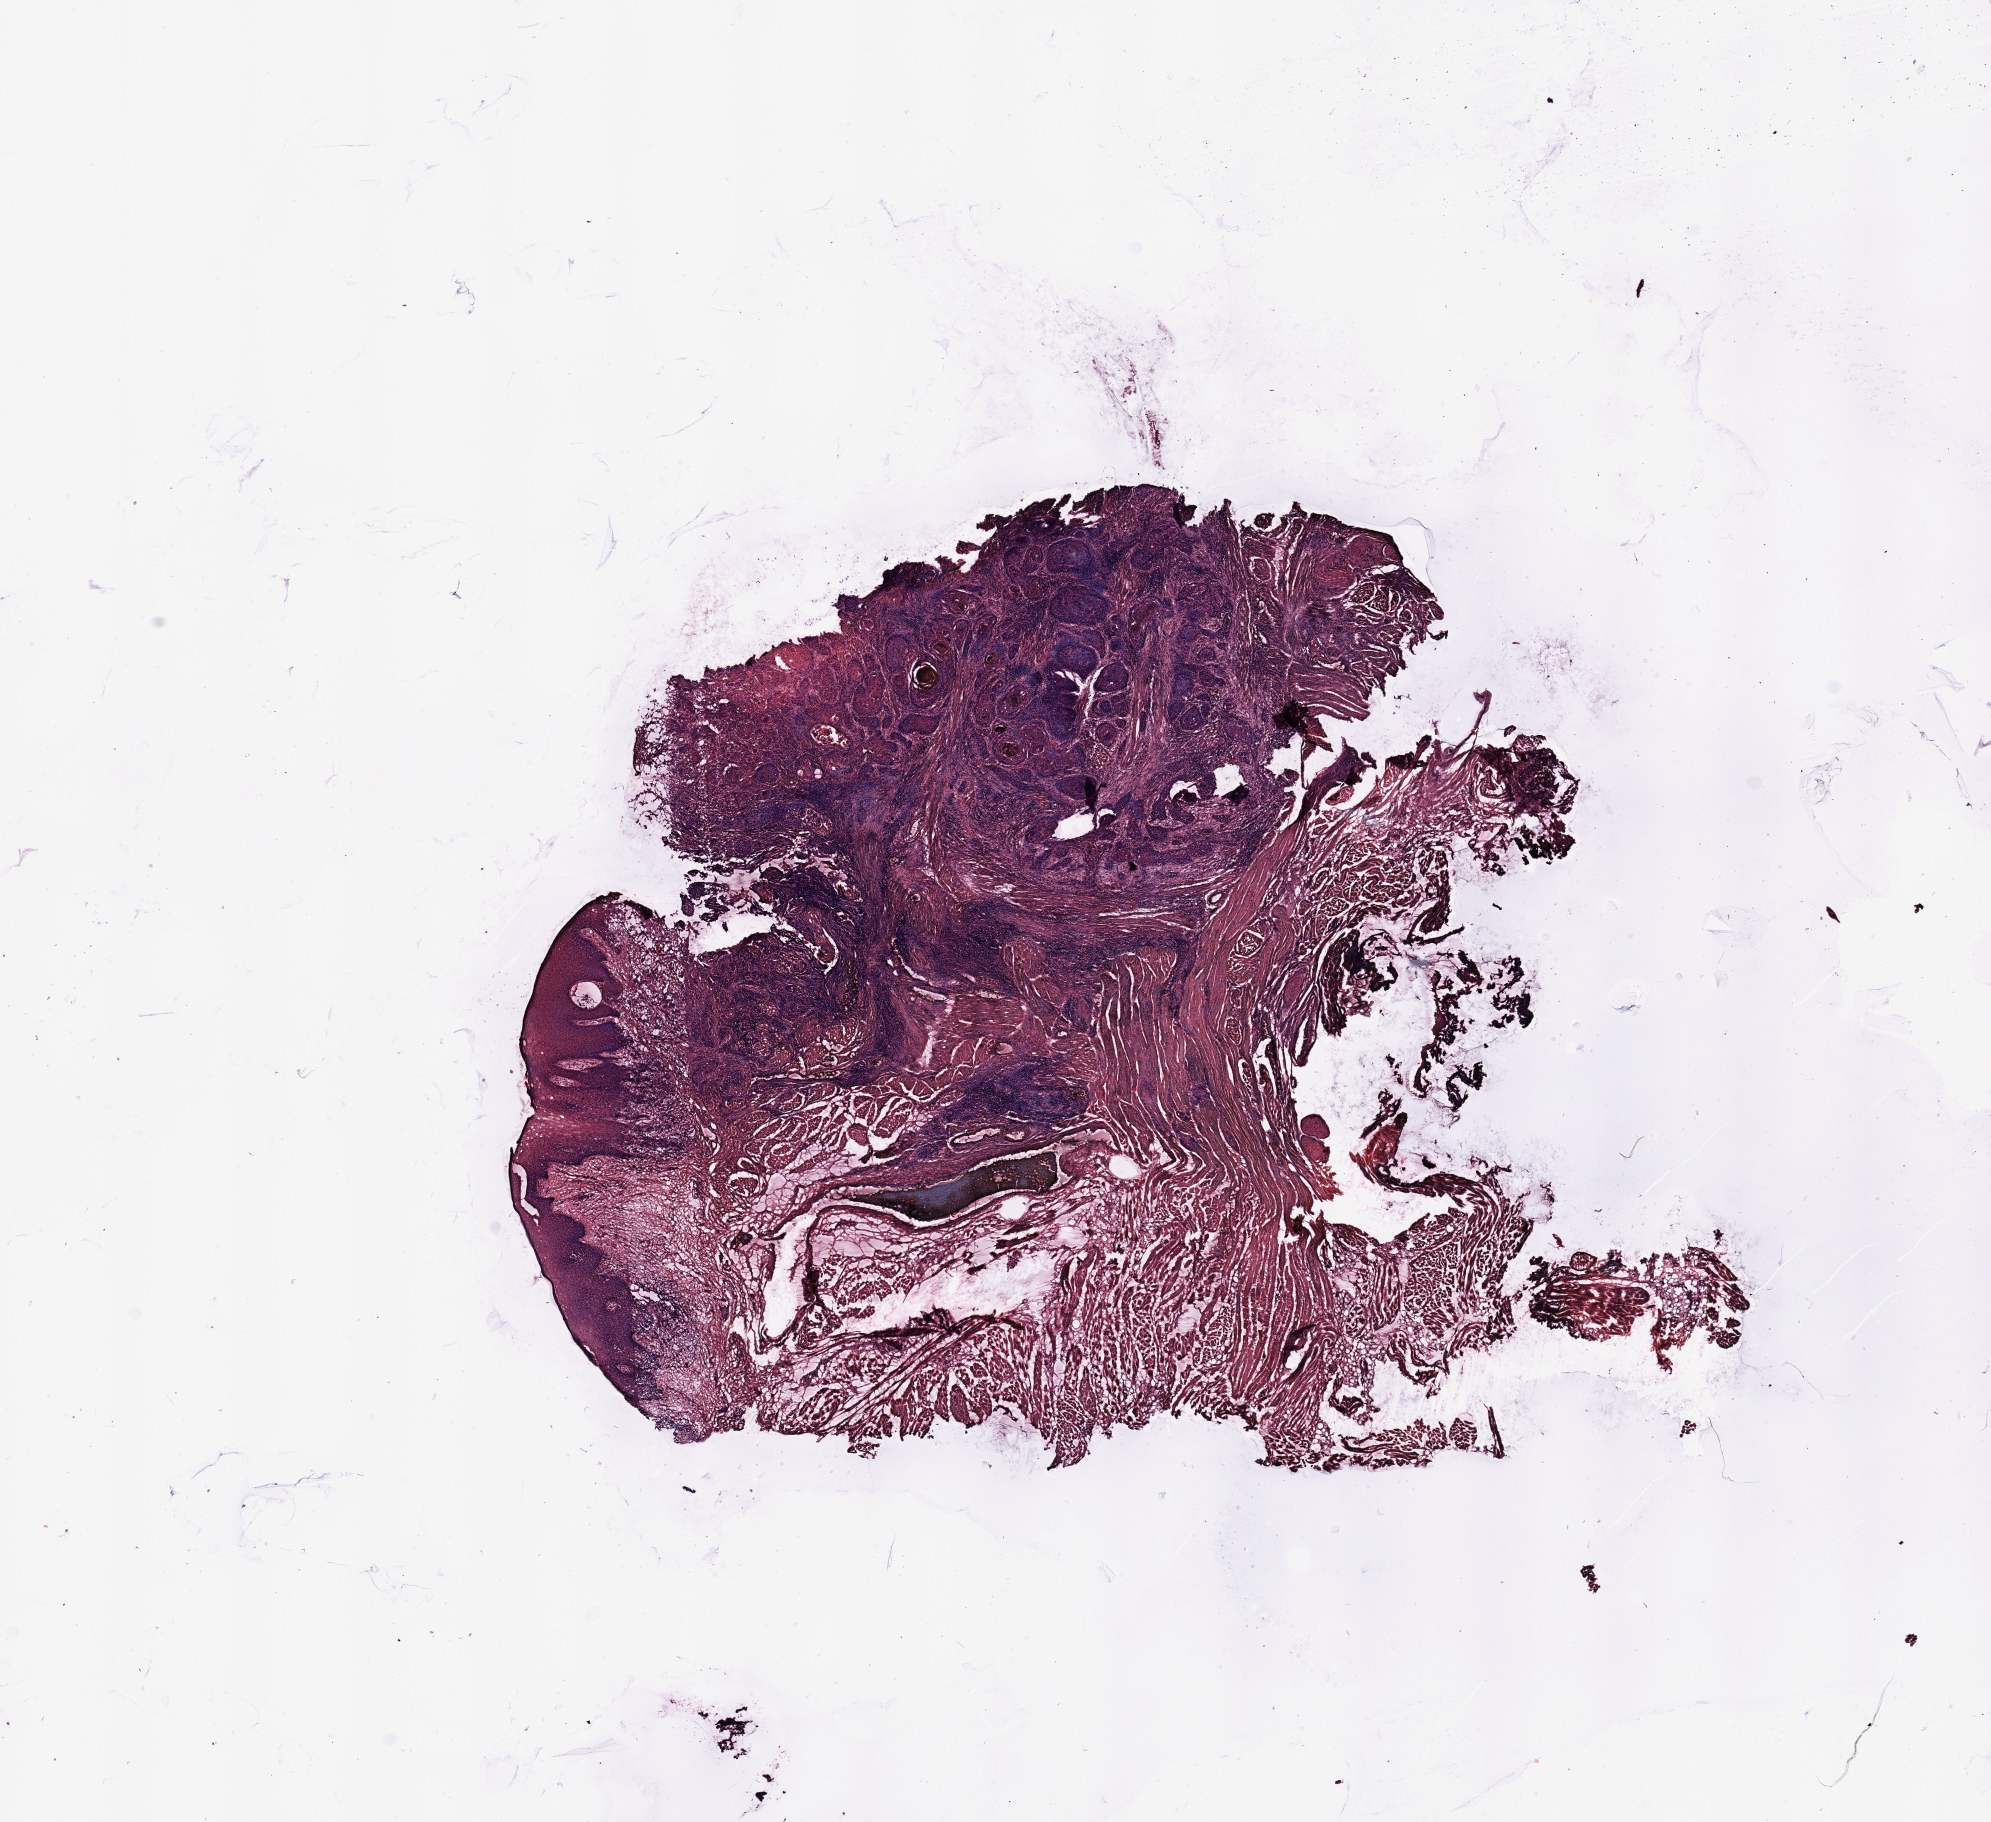
H&E whole-slide image — shown as a low-resolution overview of the whole scanned area (about 15.8 x 14.4 mm, acquisition: 20x scan). Head and neck, tissue type not recorded. Male, 67 y/o.
Patient diagnosis: Squamous cell carcinoma, NOS.